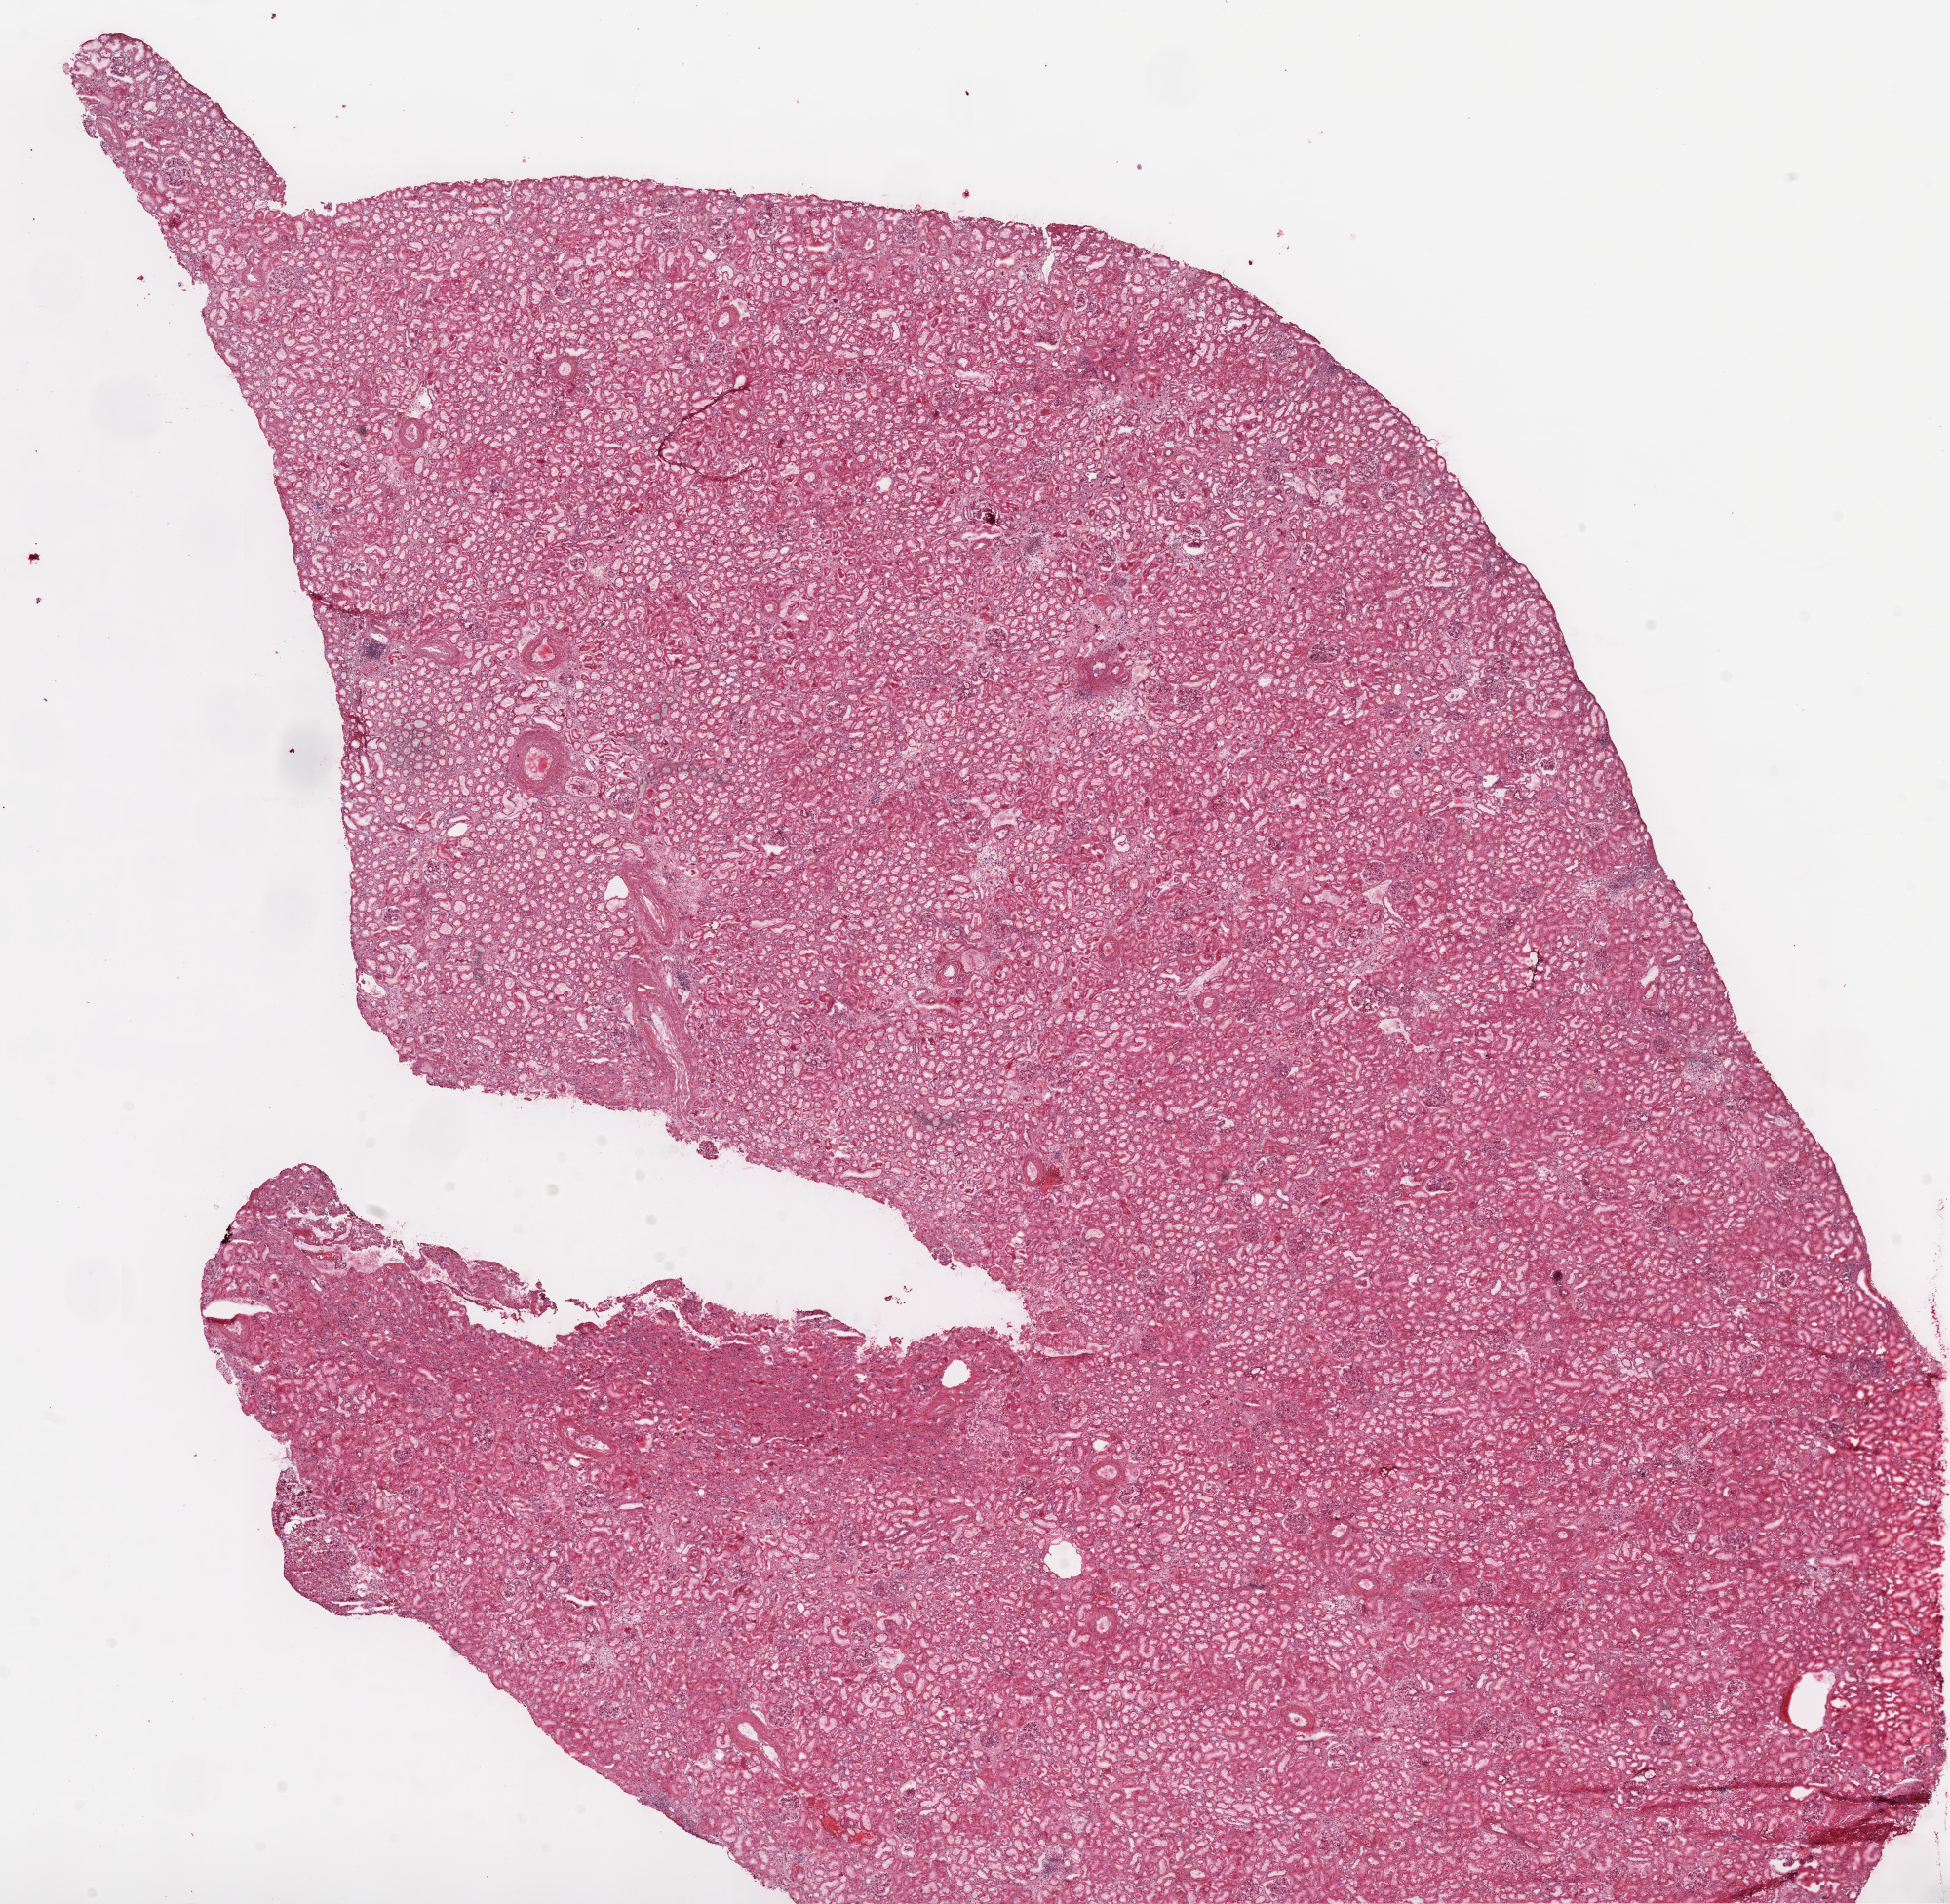
Whole-slide histology image, H&E — whole scanned area (about 16.0 x 15.7 mm, slide scanned at 20x) shown as a low-resolution overview, frozen section from the top of the tissue portion, sample: solid tissue normal (non-tumour tissue), kidney. Male, age 75 years at initial diagnosis.
This section: solid tissue normal sample (biorepository sample class). Patient diagnosis: Clear cell adenocarcinoma, NOS.